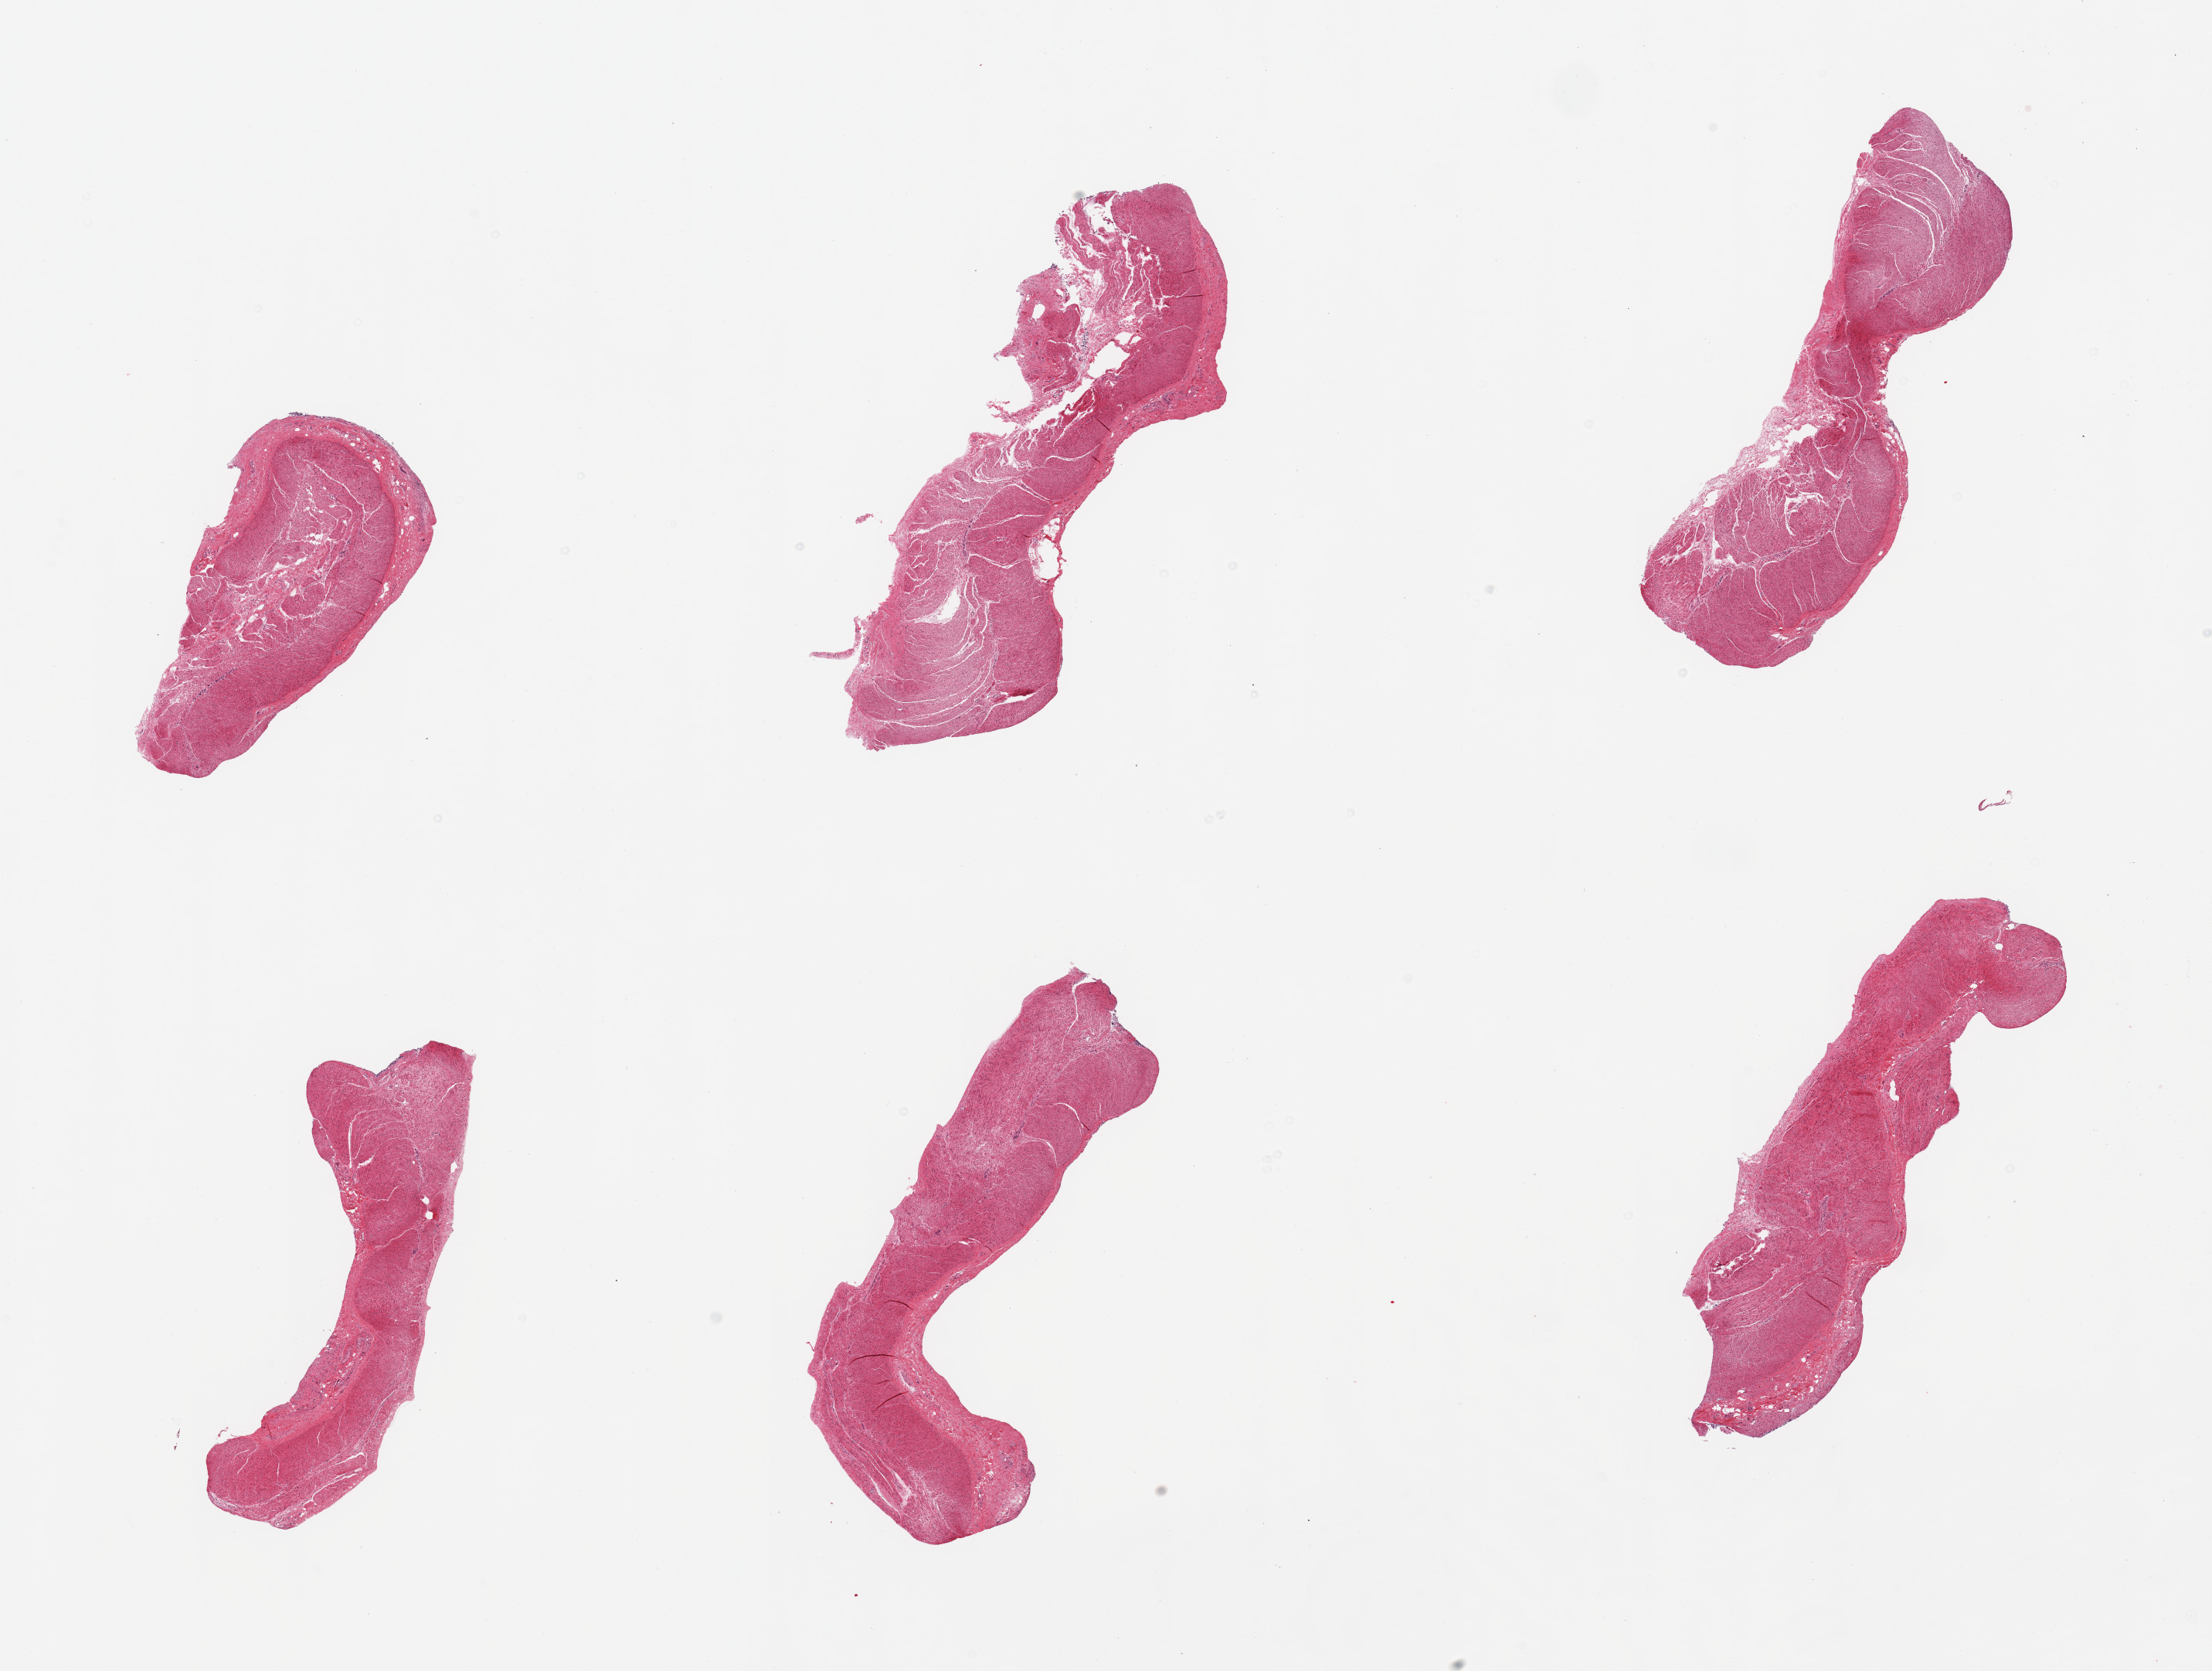
Digitized haematoxylin and eosin-stained section, whole scanned area (about 22.6 x 17.1 mm, slide scanned at 20x) shown as a low-resolution overview; PAXgene-fixed paraffin-embedded (PFPE) section; section of sigmoid colon (target tissue); tissue donor sample. Male donor.
* review note (as recorded): 6 pieces, confirmed target muscularis